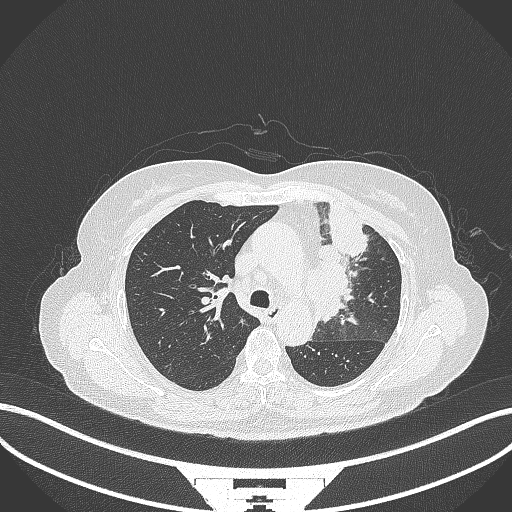
Chest CT, one axial slice; slice 229 of 382 in the series (ordered by position); reconstruction kernel B70f; lung window (W 1500 / L -600 HU); 1 mm slice thickness; 512 × 512 image matrix, field of view 400 × 400 mm. Female patient, age 64 years. From the clinical record (not read from this slice): clinical TNM (as recorded): T2a N2 M0.
Structures marked on this image (bounding box drawn by a radiologist):
- lung tumour (recorded histology: adenocarcinoma): bounding box <305,219,380,325> (left, top, right, bottom; pixels)